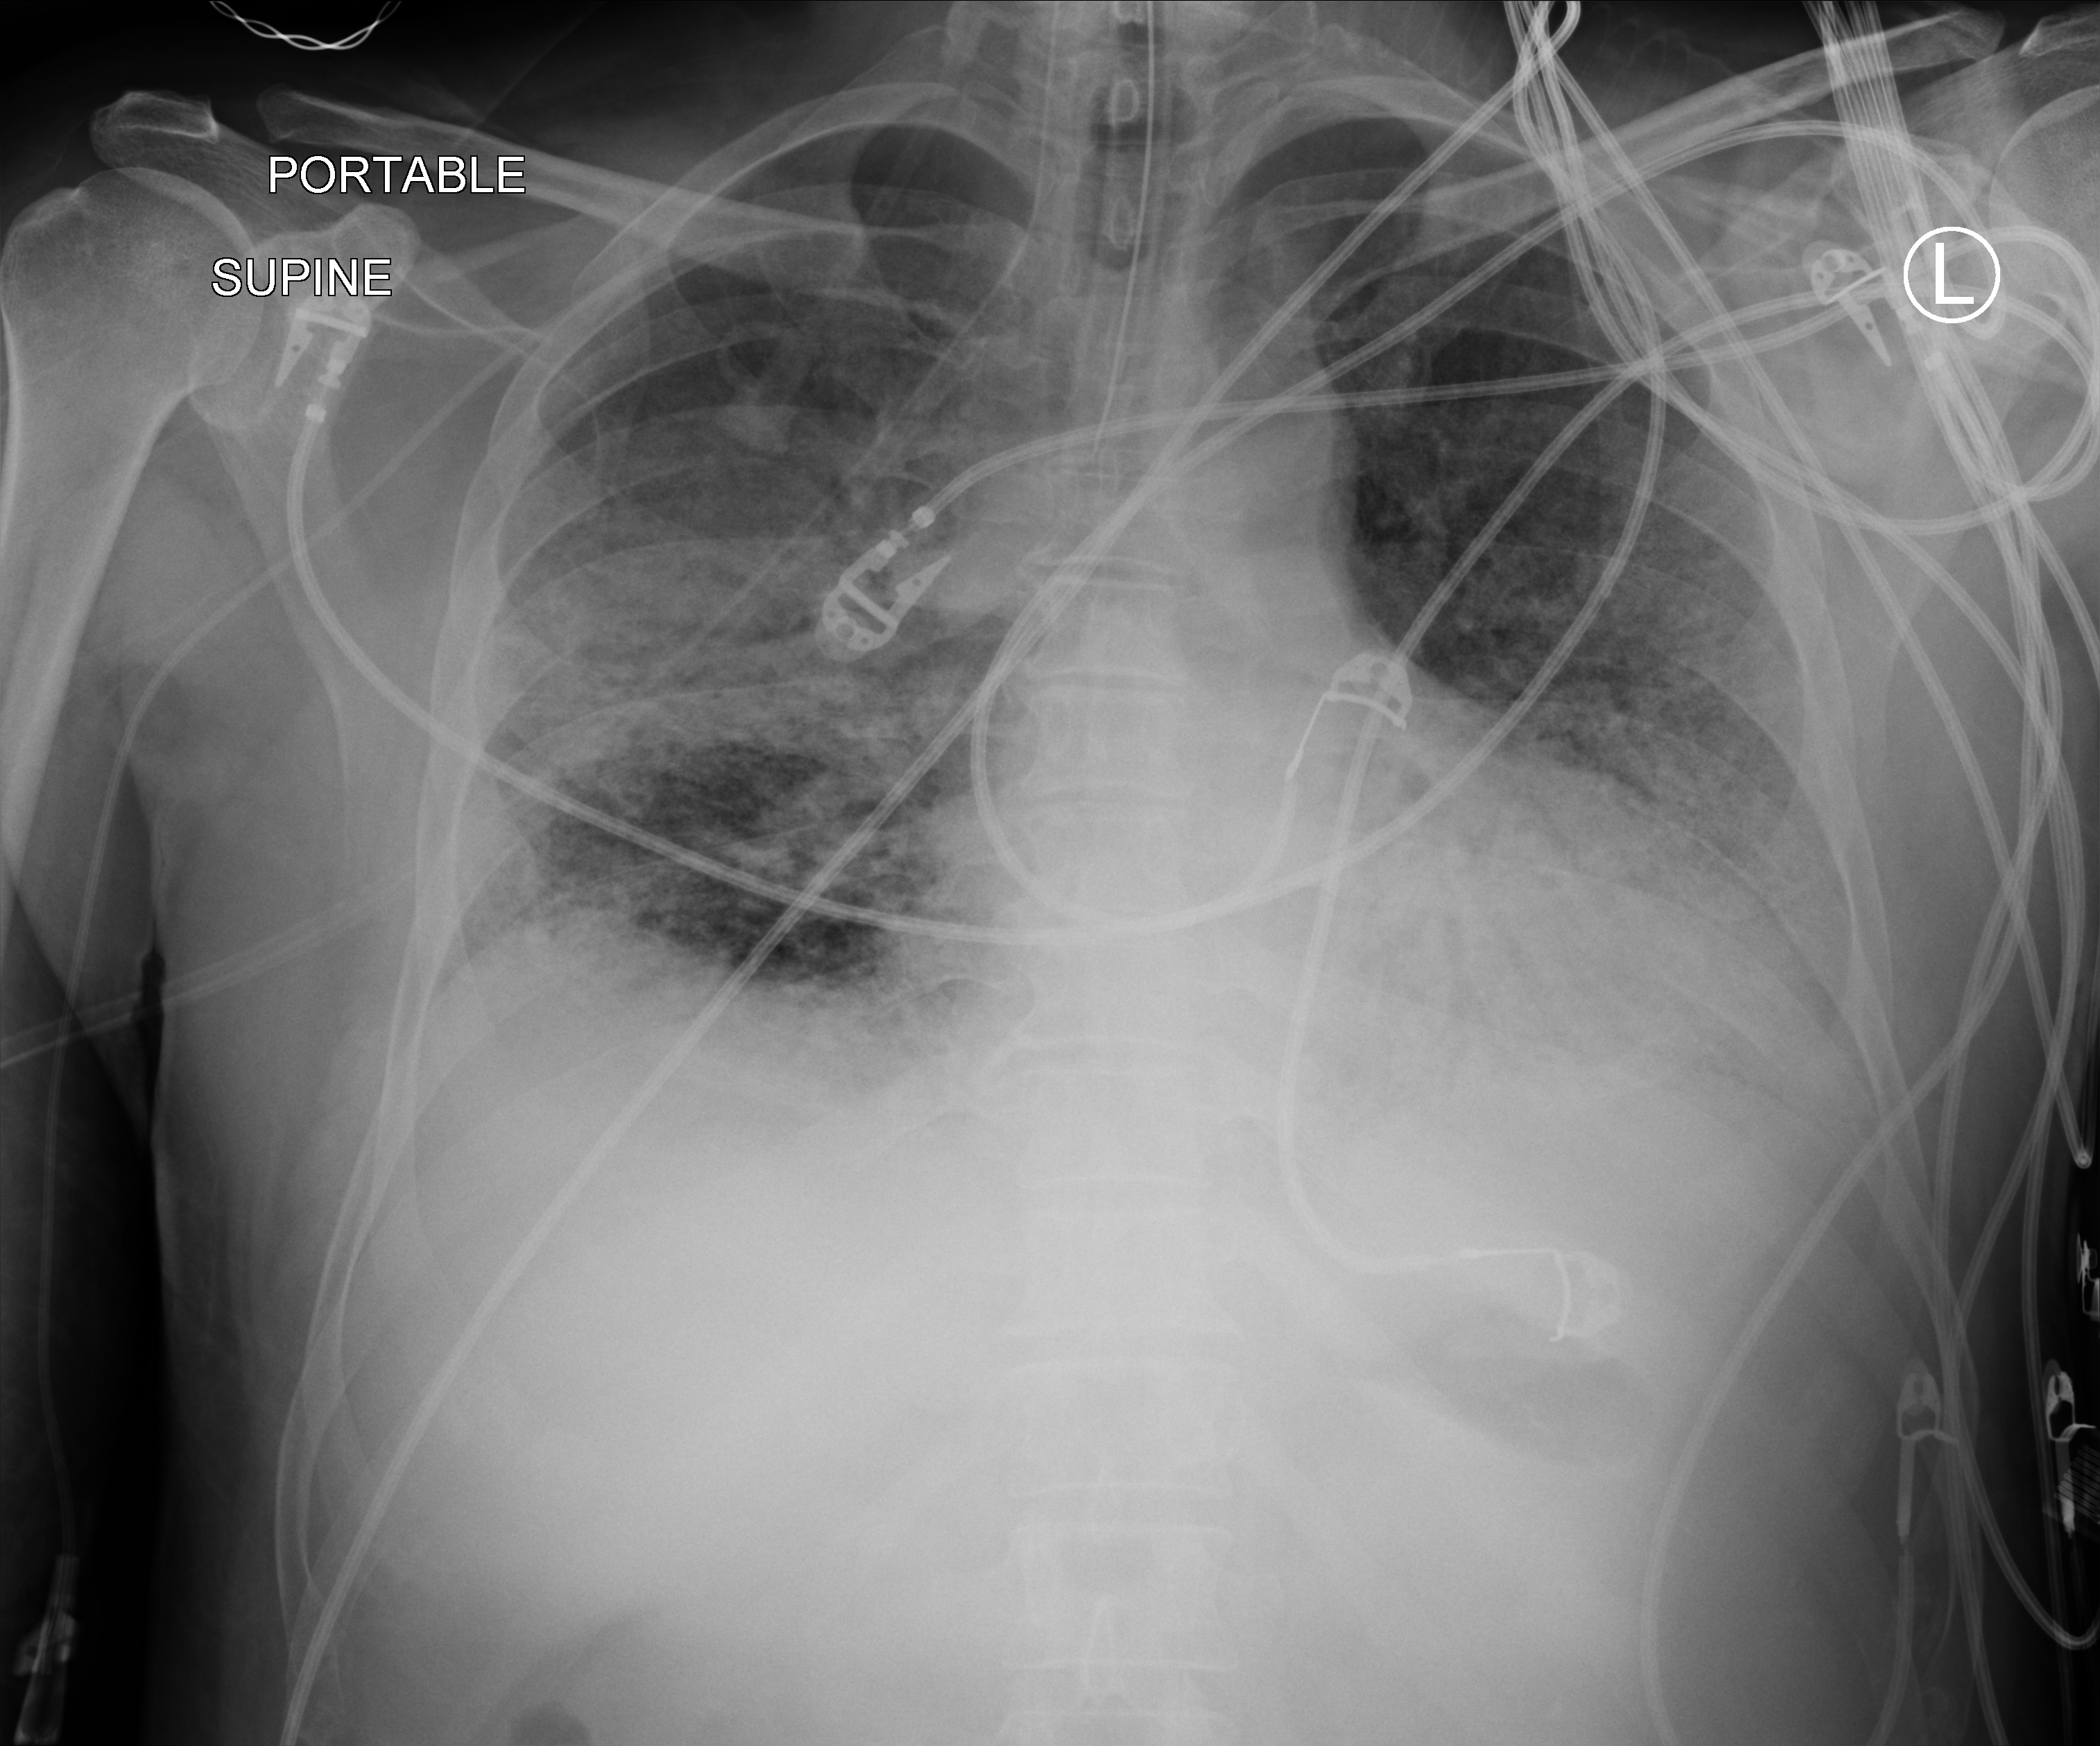
Chest X-ray (portable). Male patient hospitalised with COVID-19, age 18–59 years.
From the hospital-stay record, not from the radiograph (when in the stay this image was taken is not recorded):
- length of hospital stay: 42 days